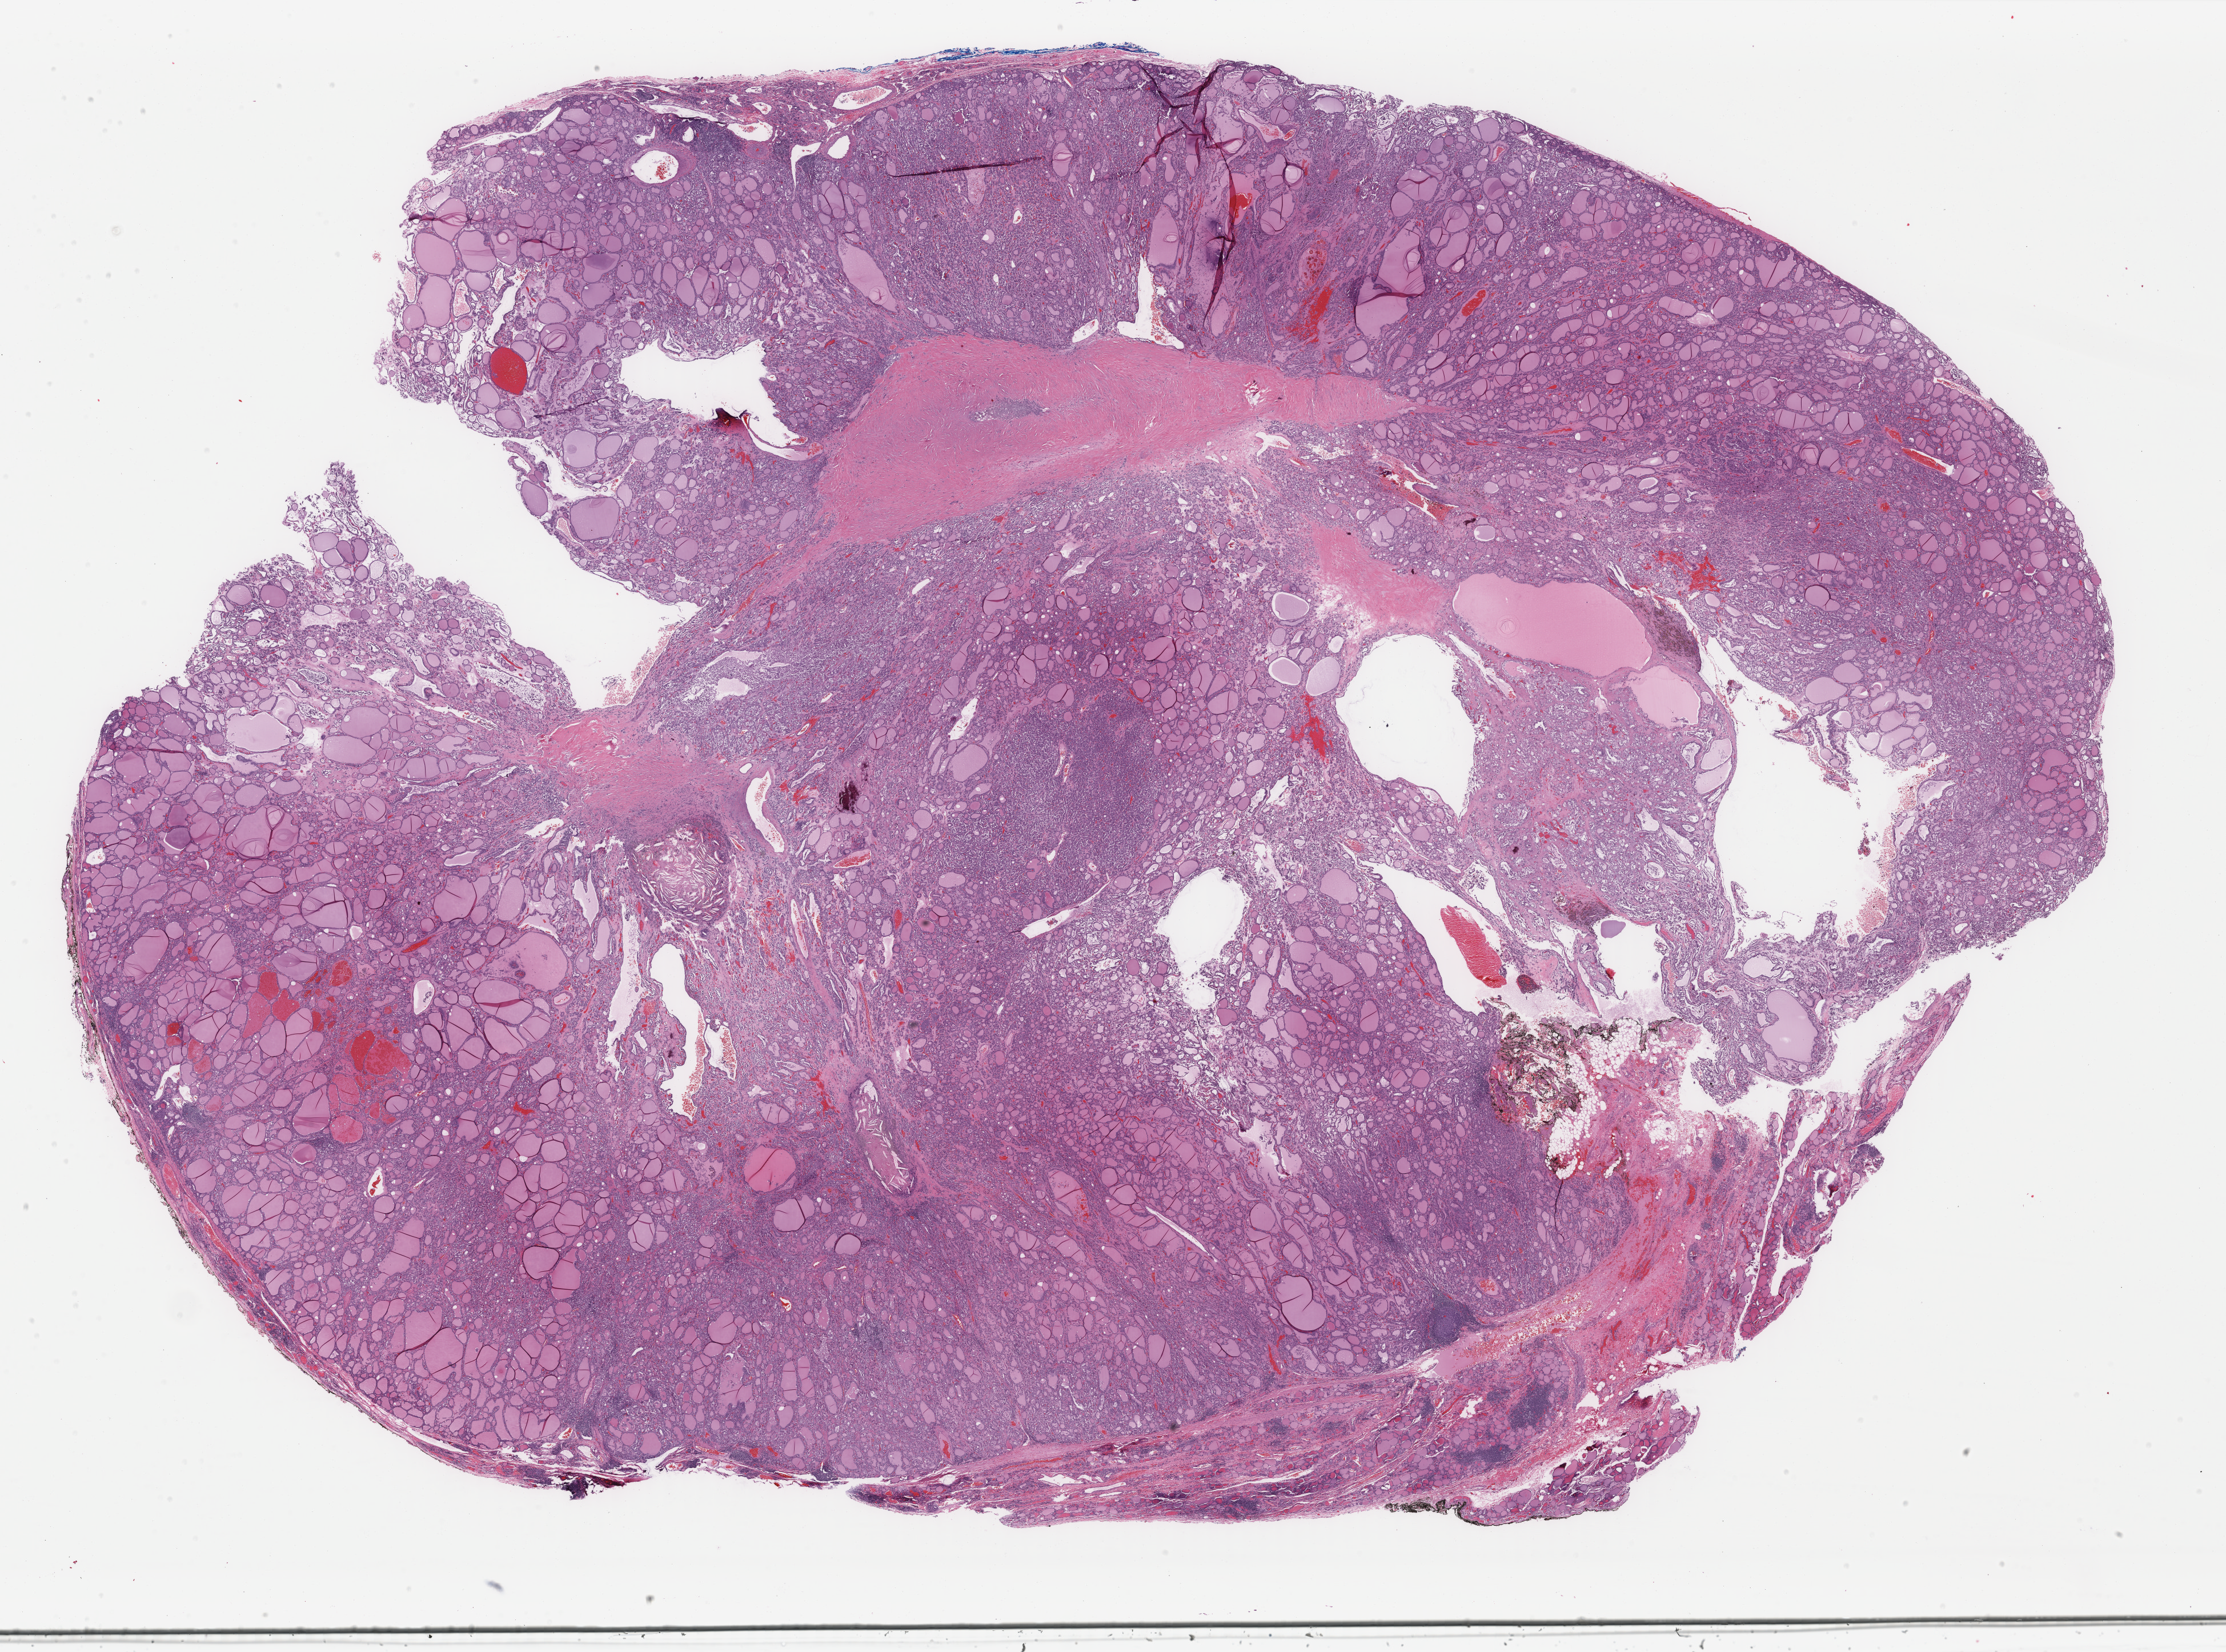
Whole-slide histology image, Hematoxylin and eosin (H&E) stained, low-resolution overview of the scanned area, about 30.9 x 23.0 mm (acquisition: 40x scan). Formalin-fixed paraffin-embedded (FFPE) diagnostic section. Thyroid, primary tumour sample. Patient: female, age at initial diagnosis 57 years.
* diagnosis: Papillary carcinoma, follicular variant (thyroid gland)
* laterality: right
* AJCC pathologic stage: III
* TNM: T3 N0 M0
* lymph nodes positive (case pathology): 0 of 1 examined